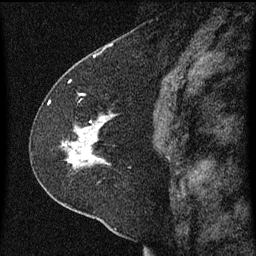
Breast MRI (dynamic contrast-enhanced), one sagittal slice. Position 34 of 60 along the scan axis. Dynamic contrast-enhanced series, image 2 of 3 at this slice position (ordered by acquisition). 1.5 T. TE 4.2 ms, TR 8 ms. 2 mm slice thickness. 256 × 256 image matrix, field of view 180 × 180 mm. Patient: female, 47 years.
Annotated regions visible in this slice (semi-automatic segmentation, software-assisted and operator-edited):
- analysis volume of interest (the breast-tissue region the enhancement analysis was run in; not a lesion): box from (x=36, y=96) to (x=121, y=213) px
- tumour enhancement mask (voxels above the 70 % enhancement threshold inside the analysis volume of interest): (x=63, y=116)–(x=104, y=165)